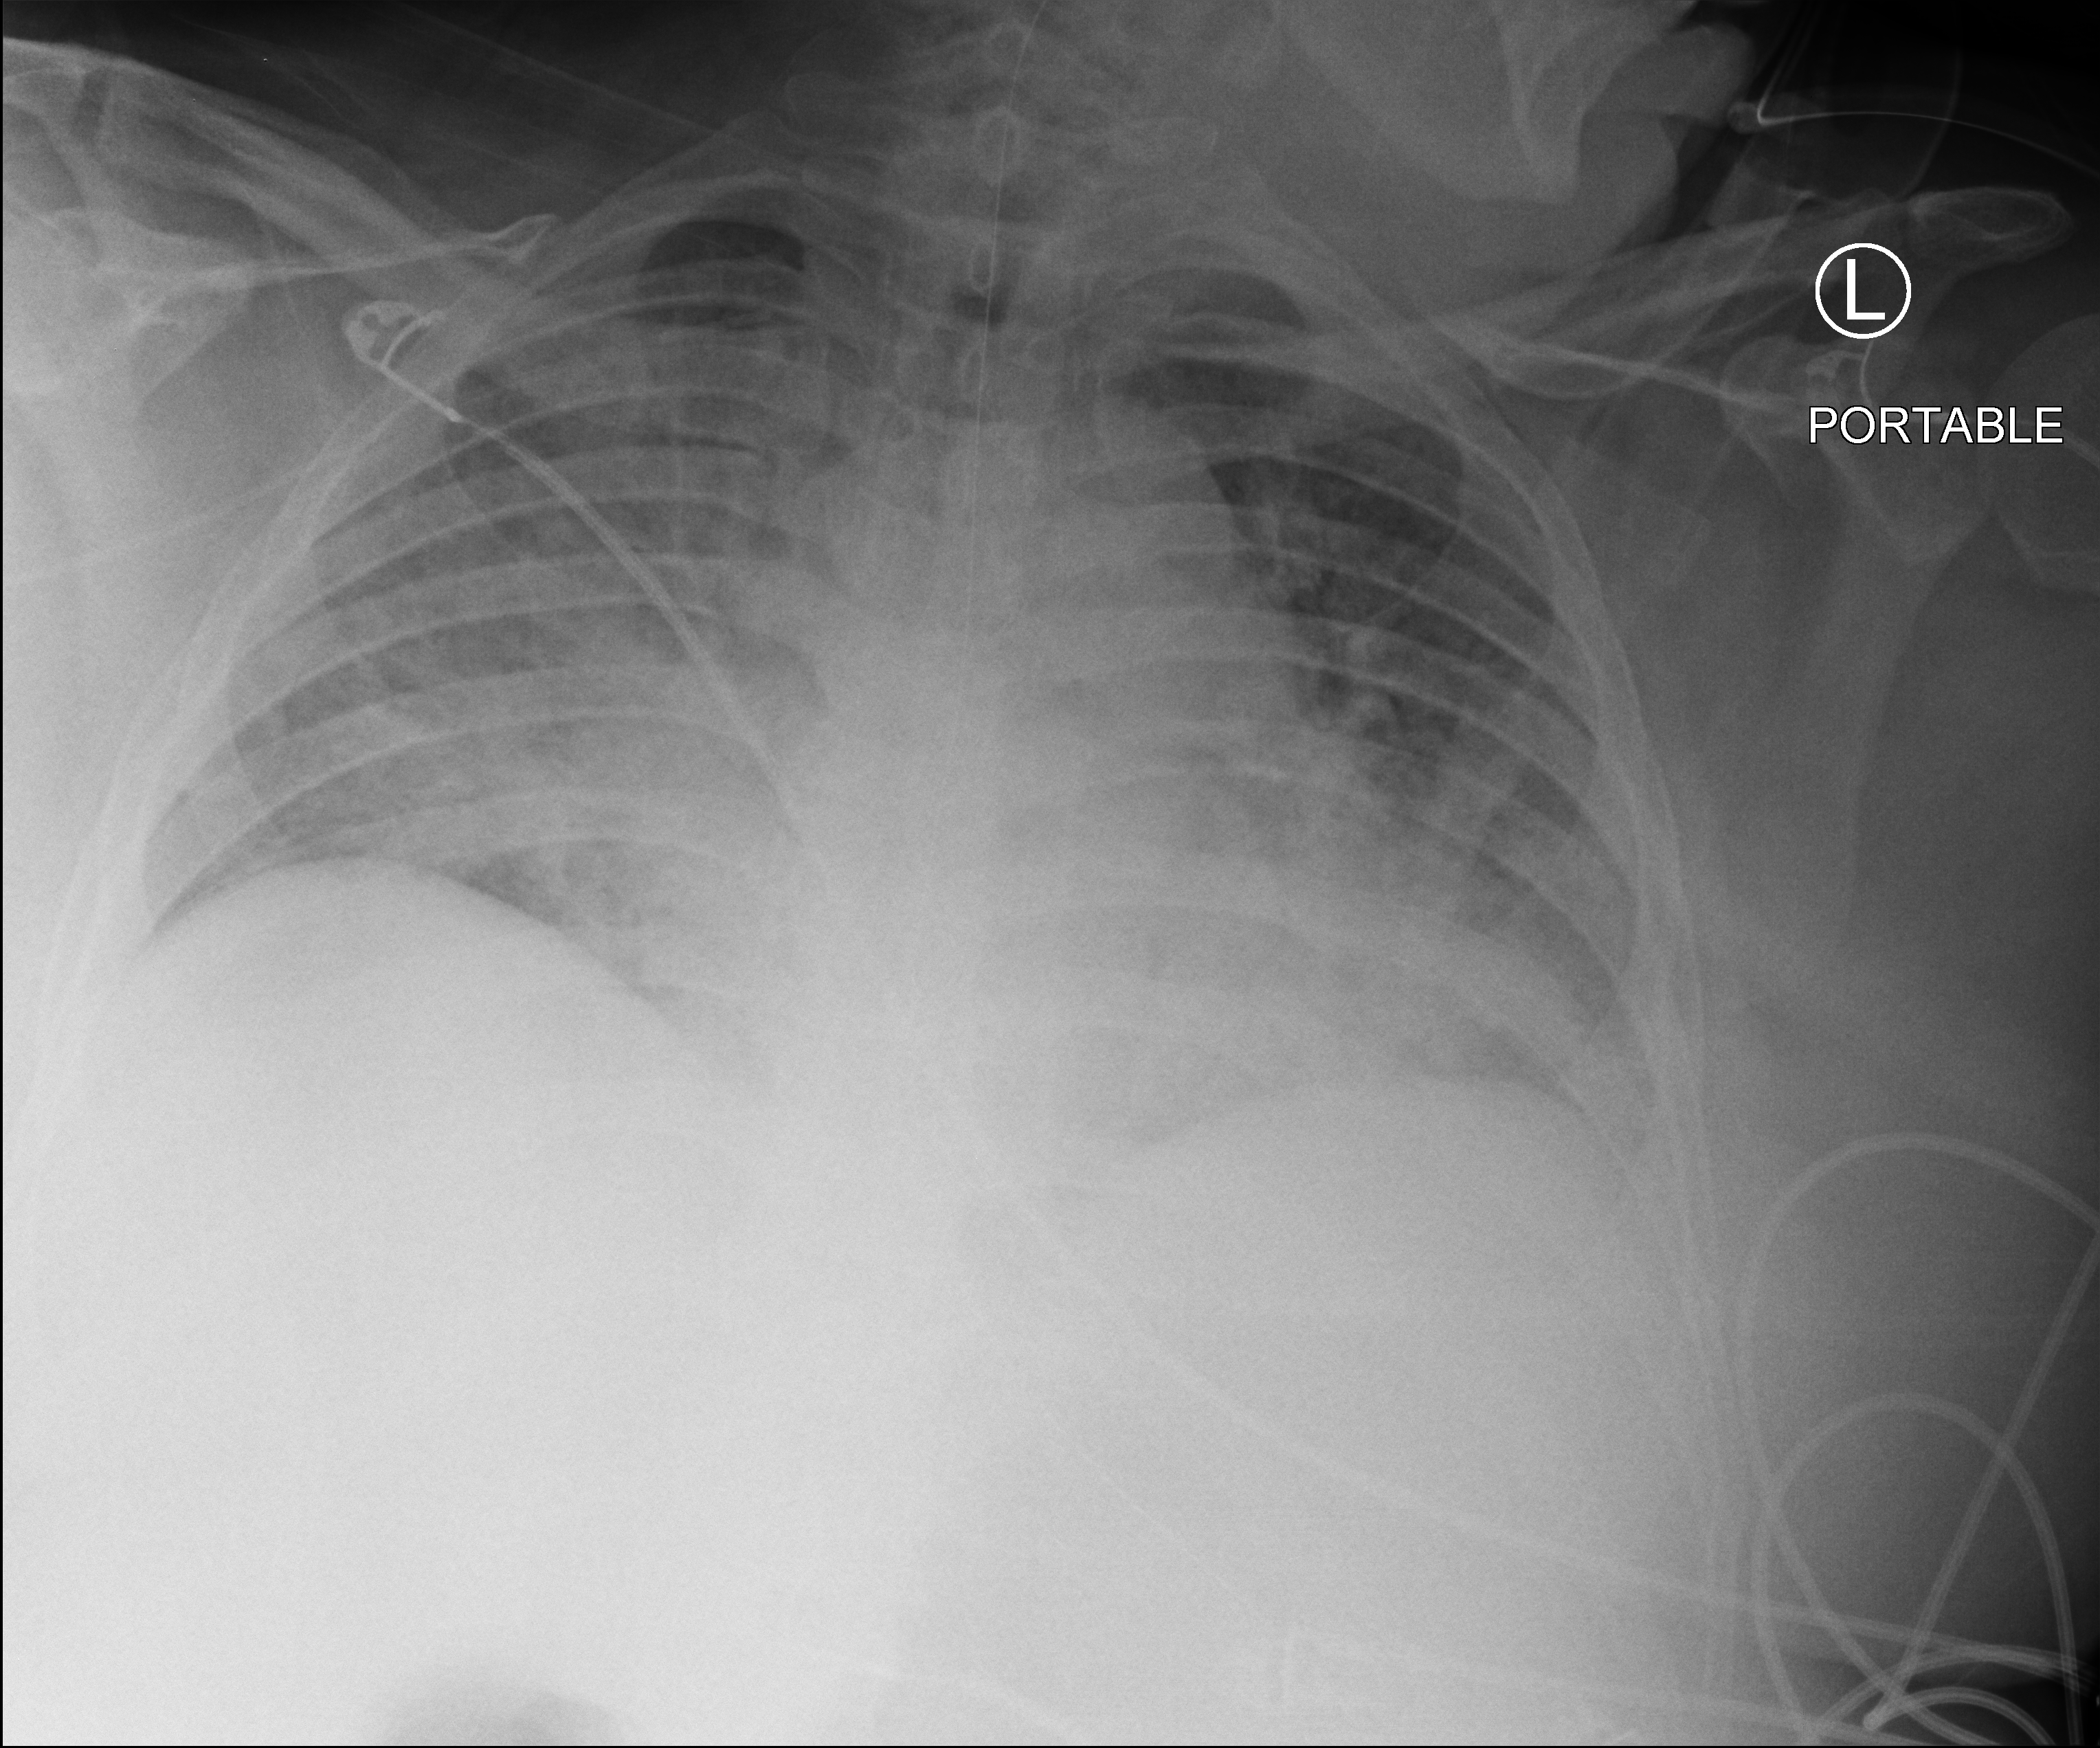
Bedside chest radiograph (computed radiography); anteroposterior (AP) projection. Male patient hospitalised with COVID-19, age 18–59 years.
Admission-level facts for this patient (not findings on this image; timing relative to this image not recorded):
- mechanically ventilated during this hospital stay: yes
- admitted to intensive care during this hospital stay: yes
- diabetes (admission record): yes